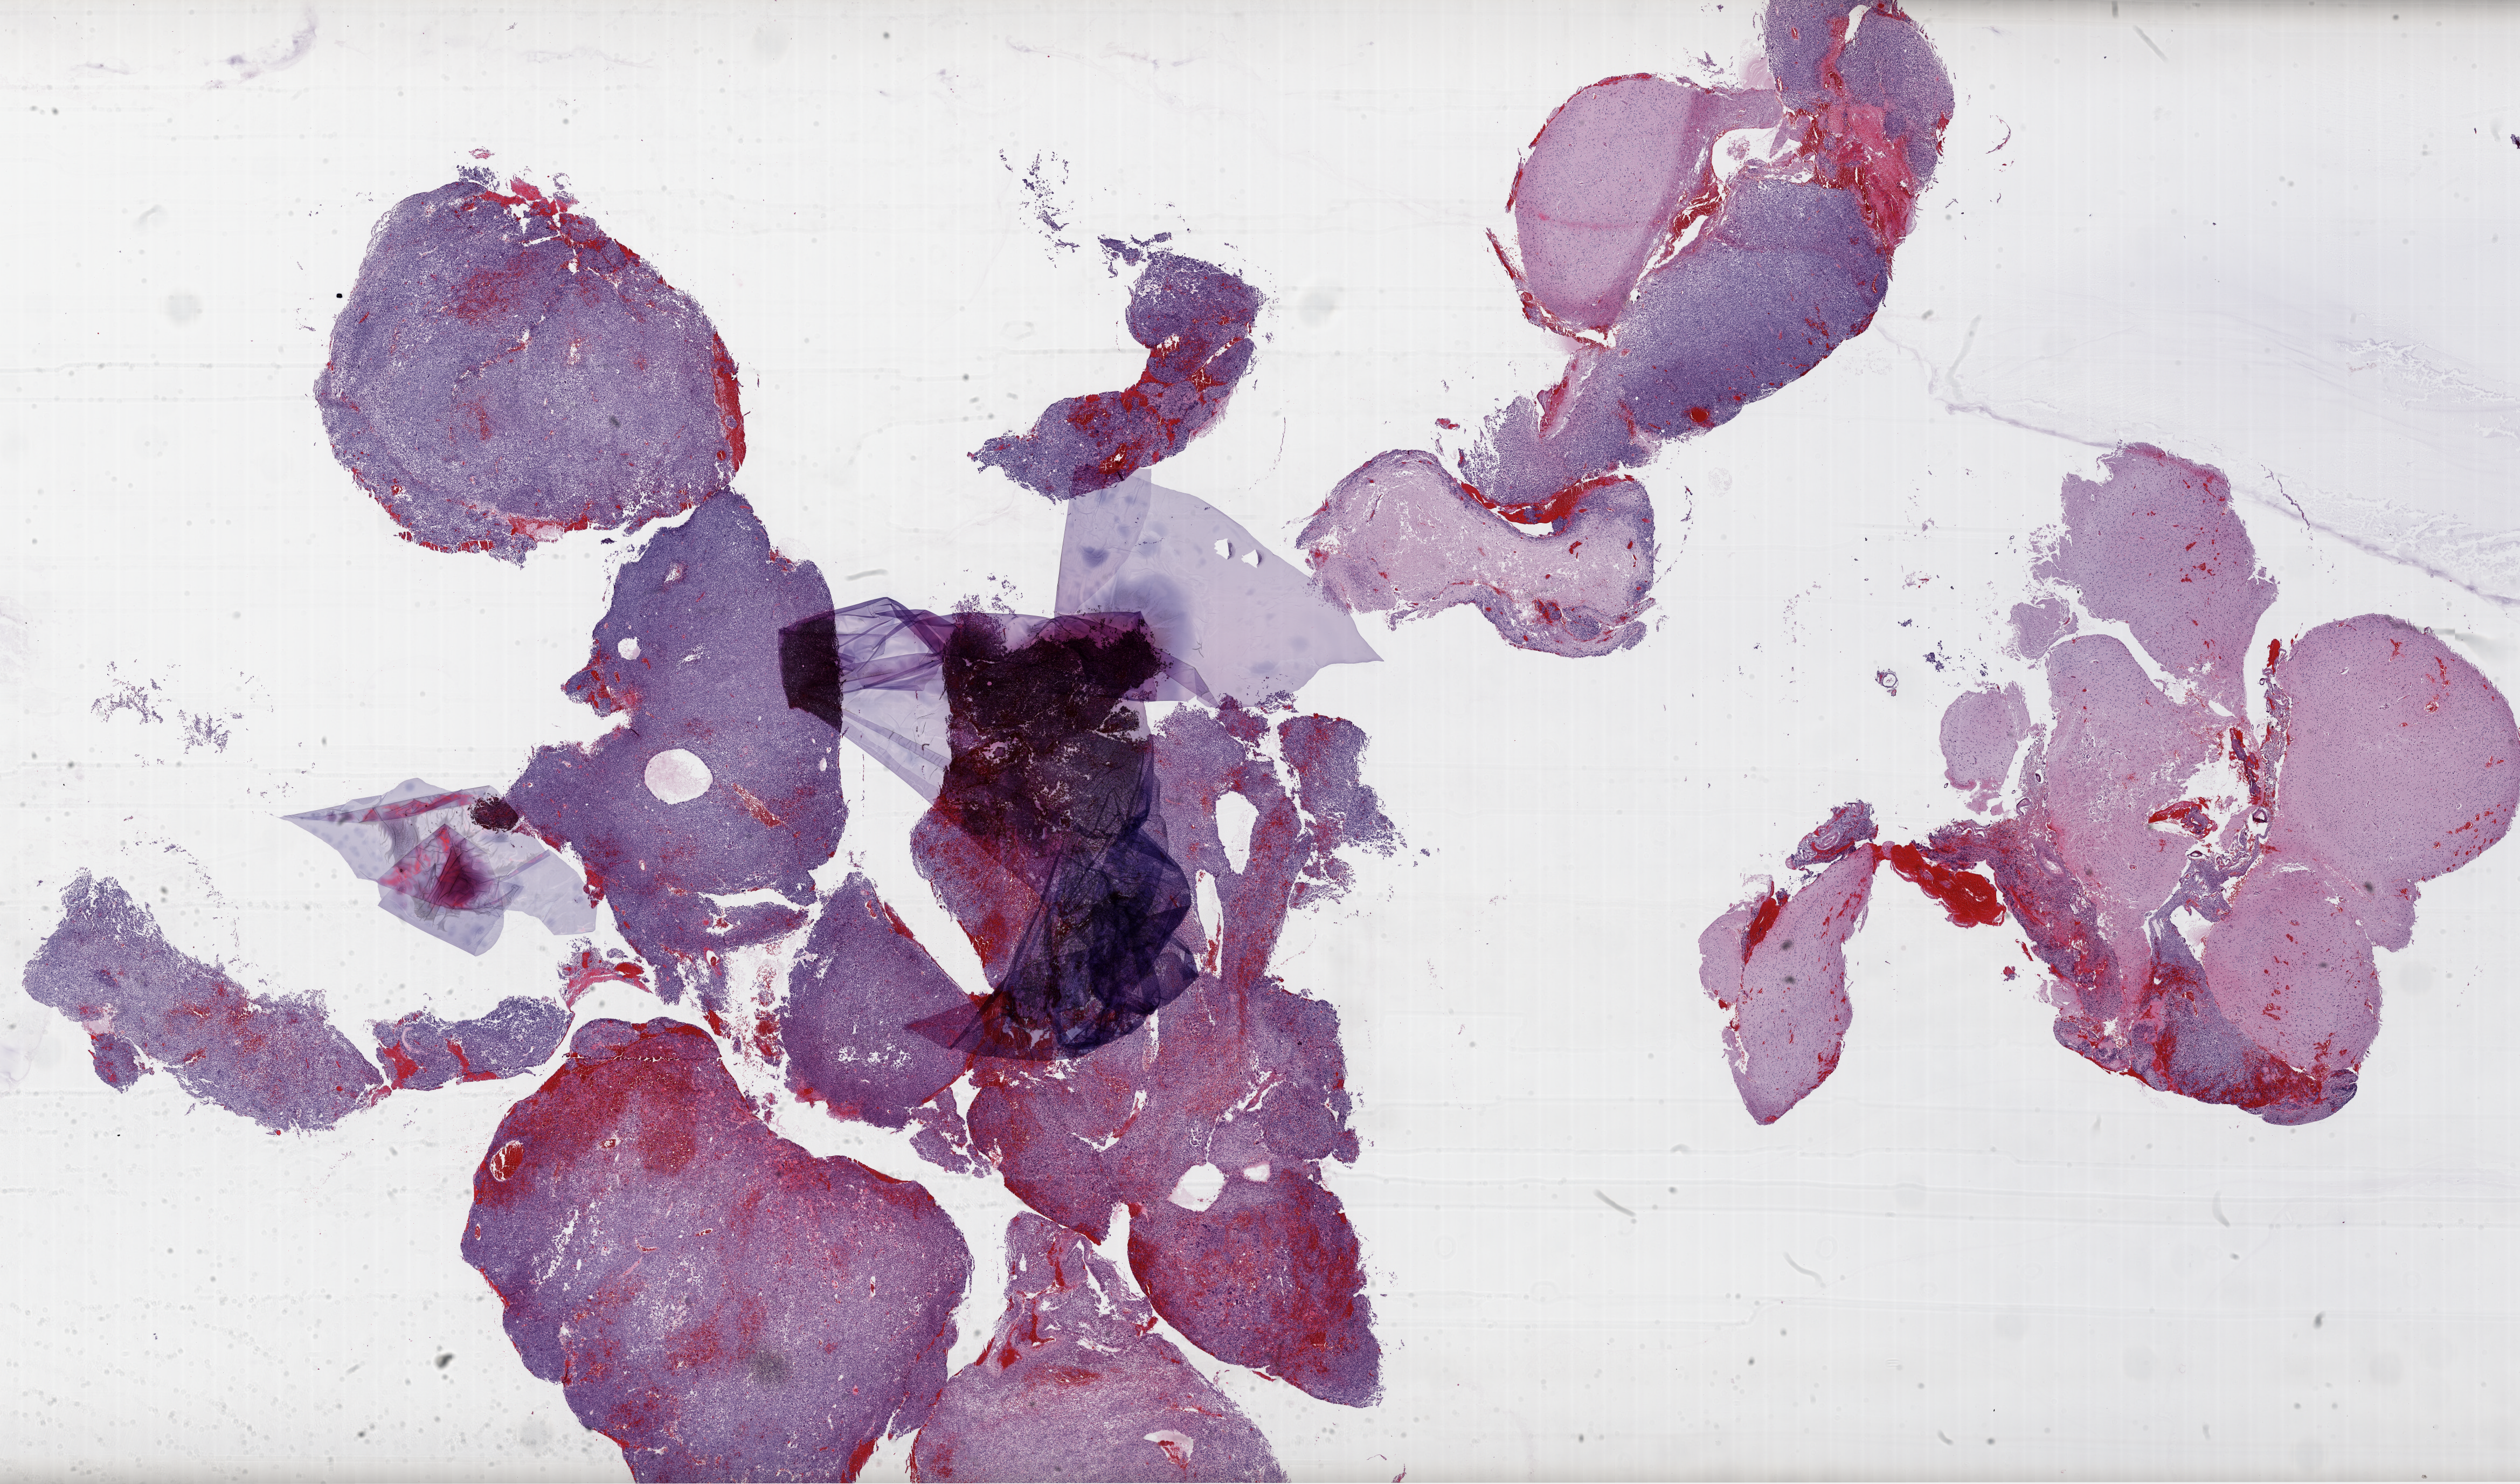
Whole-slide histology image, Hematoxylin and eosin (H&E) stained — whole scanned area (about 37.7 x 22.2 mm) shown as a low-resolution overview, FFPE section, brain, primary tumour sample. Female, age 74 years at initial diagnosis.
Histologic diagnosis: Glioblastoma.